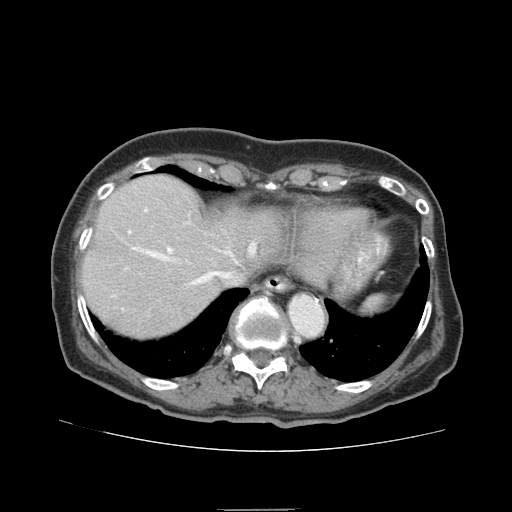
Contrast-enhanced abdominal CT (liver protocol), one axial slice. Position 68 of 95 along the scan axis. Reconstruction kernel STANDARD. Soft-tissue window (W 400 / L 40 HU). 2.5 mm slice thickness. 512 × 512 image matrix, field of view 360 × 360 mm. From the clinical record (not read from this slice): diagnosis: hepatocellular carcinoma (patient treated with transarterial chemoembolisation; whether this scan precedes or follows treatment is not stated here); TNM stage (as recorded): Stage-IVA; Child-Pugh class: B; tumour differentiation: moderately differentiated; tumour nodularity: uninodular.
Annotated regions visible in this slice (semi-automatically segmented with operator editing):
- liver parenchyma outside the tumour (the mass and vessels are separate outlines, so this box may not span the whole liver): bounding box (x1, y1, x2, y2) in pixels: (82, 174, 280, 336)
- liver vessels: (122, 208, 256, 310)